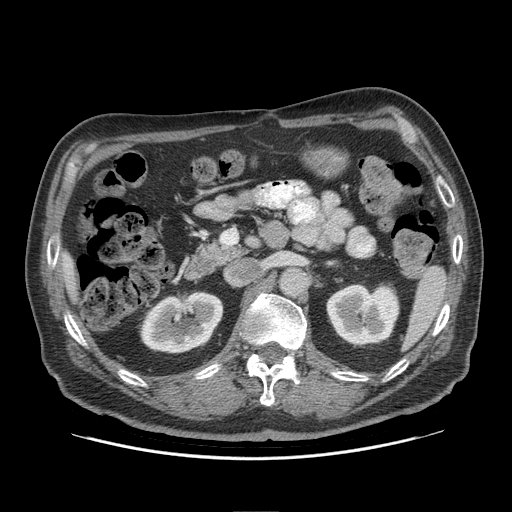
Contrast-enhanced abdominal CT (liver protocol), one axial slice. Position 44 of 95 along the scan axis. Soft-tissue window (W 400 / L 40 HU). 512 × 512 image matrix. Case-level facts recorded for this patient, not image findings: diagnosis: hepatocellular carcinoma (patient treated with transarterial chemoembolisation; whether this scan precedes or follows treatment is not stated here); TNM stage (as recorded): Stage-IVB; Child-Pugh class: A; tumour differentiation: well differentiated; tumour nodularity: uninodular.
Outlined on this slice (semi-automatically segmented with operator editing):
- liver parenchyma outside the tumour (the mass and vessels are separate outlines, so this box may not span the whole liver): box from (x=60, y=252) to (x=78, y=304) px